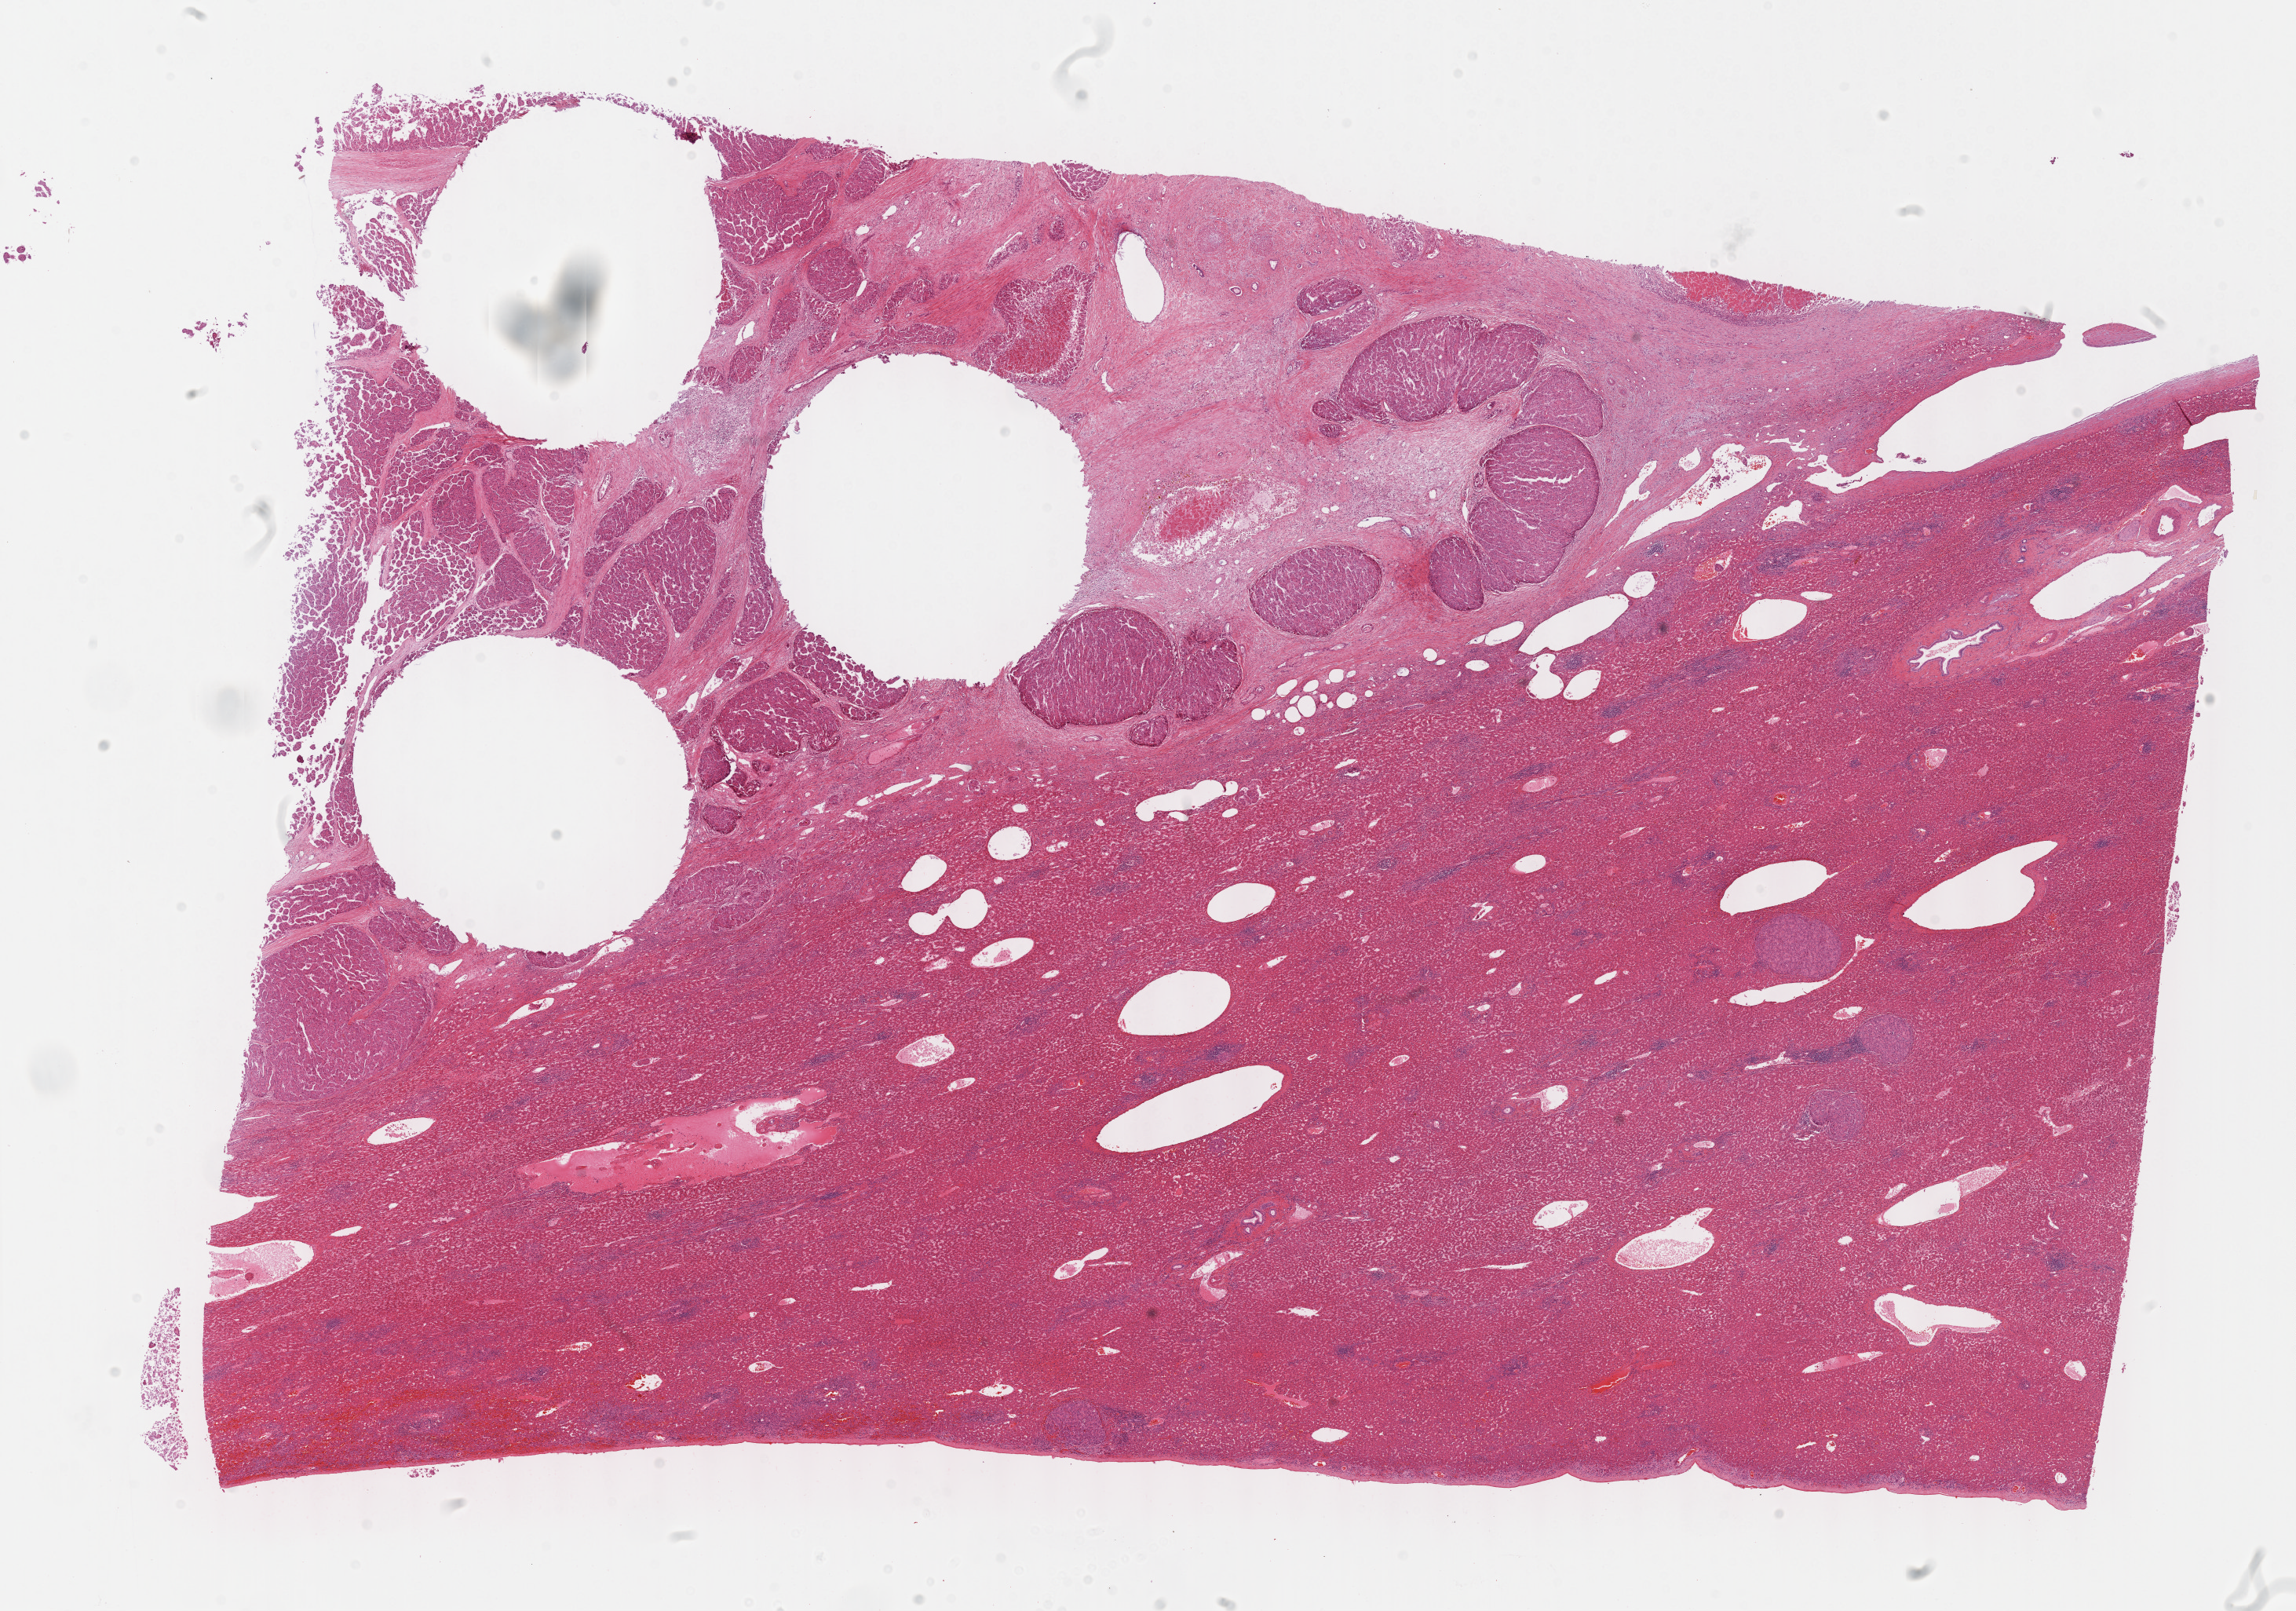
Digitized H&E tissue section (whole slide) — shown as a low-resolution overview of the whole scanned area (about 23.6 x 16.6 mm, acquisition: 40x scan). Formalin-fixed paraffin-embedded (FFPE) diagnostic section. Primary tumour sample from the liver. Male, age 48 years at initial diagnosis. Histologic grade: G4 (undifferentiated).
- TNM: T1 N0 M0
- AJCC pathologic stage: I (6th edition)
- pathologic diagnosis: Hepatocellular carcinoma, NOS